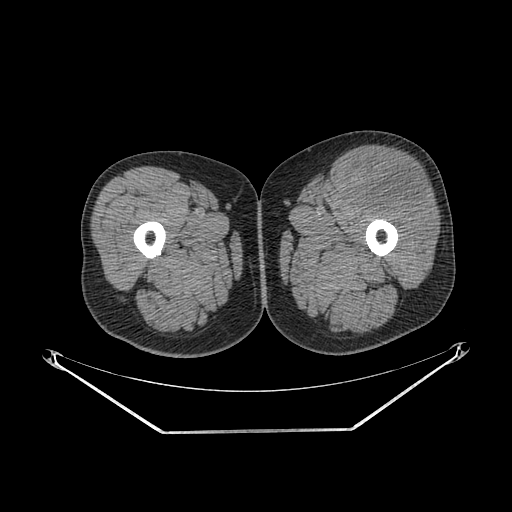
CT of an extremity soft-tissue mass (from a PET/CT study), one axial slice. Position 237 of 267 along the scan axis. Reconstruction kernel SOFT. Soft-tissue window (W 400 / L 40 HU). 3.75 mm slice thickness. 512 × 512 image matrix, field of view 500 × 500 mm. Male patient. From the clinical record (not read from this slice): histological type: extraskeletal osteosarcoma; grade: high; site of the primary tumour: thigh.
Structures marked on this image (expert contour drawn on MRI and transferred to this co-registered scan by the dataset authors):
- gross tumour volume (mass): bounding box (x1, y1, x2, y2) in pixels: (352, 158, 433, 211)